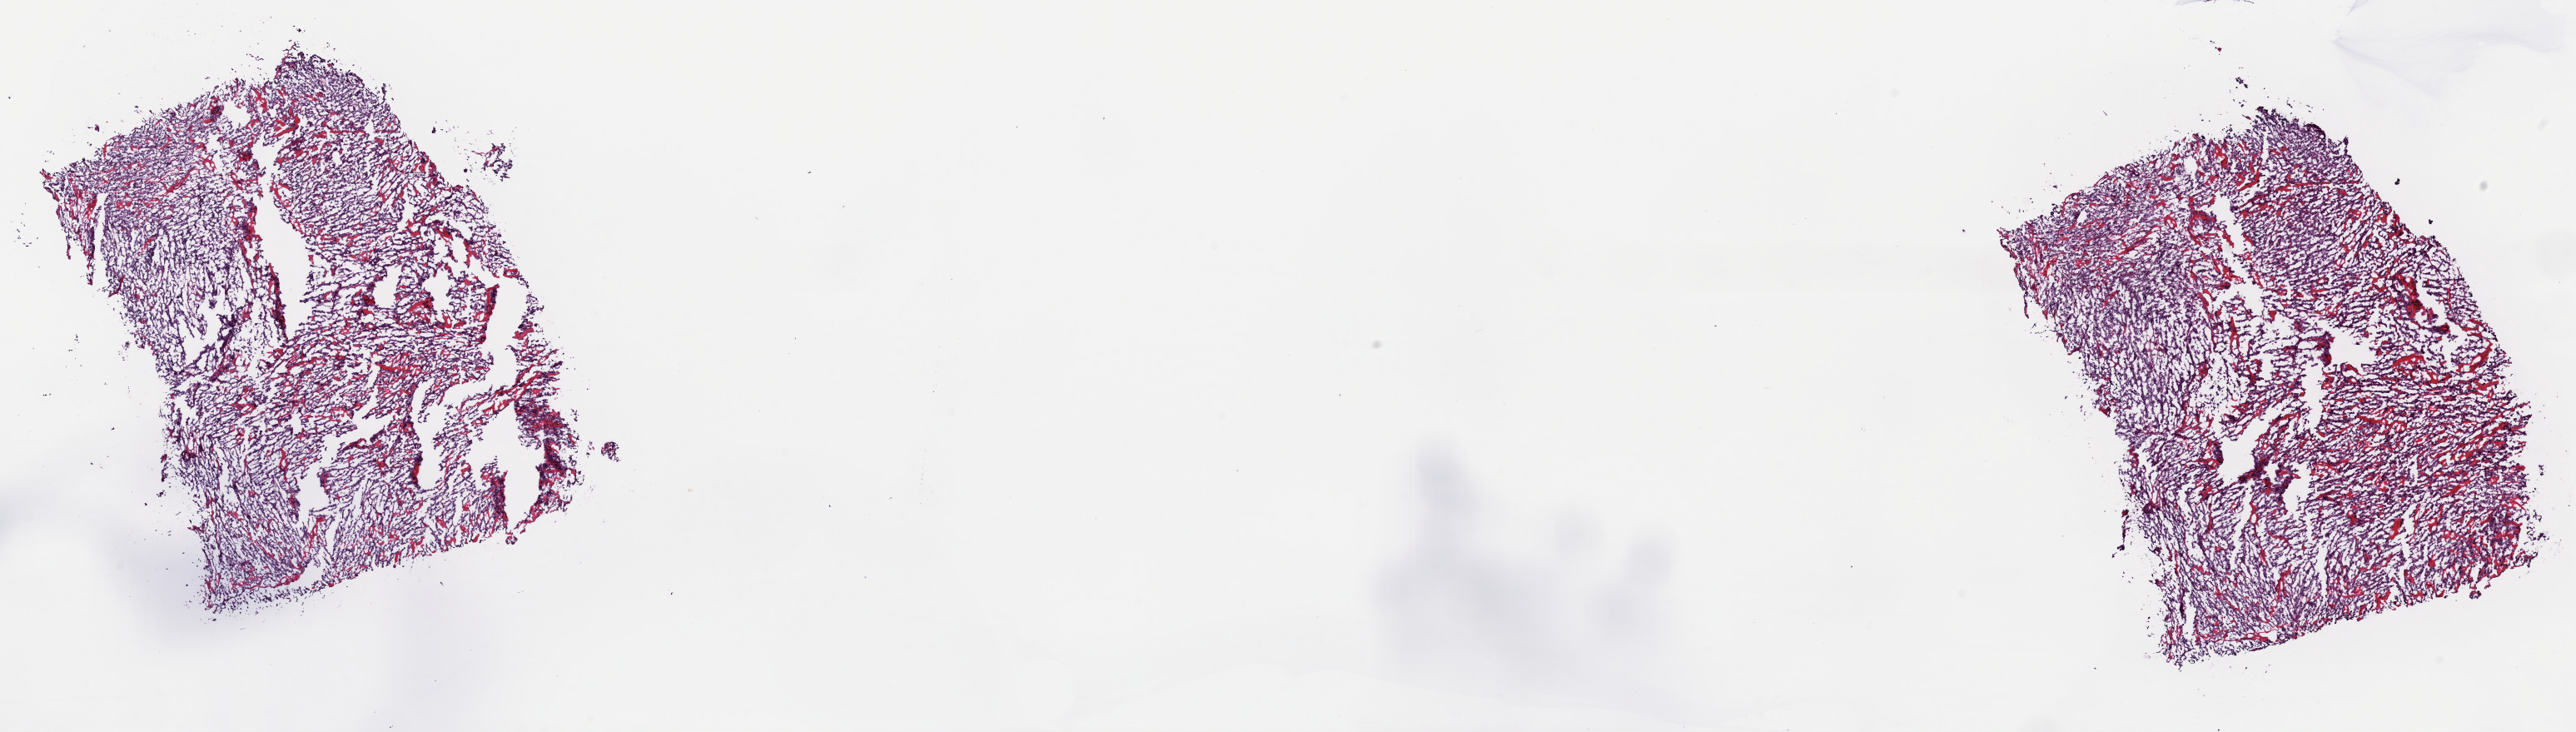
Digitized H&E tissue section (whole slide), low-resolution overview of the scanned area, about 24.4 x 6.9 mm (slide scanned at 40x); frozen section from the top of the tissue portion; skin, primary tumour sample. Male patient; age at initial diagnosis 24 years. Pathologist review of this section (percent, as recorded): tumour cells 85%, tumour nuclei 85%, normal cells 0%, stromal cells 15%, necrosis 0%. Infiltration values recorded for this section: lymphocyte infiltration 2%, monocyte infiltration 1%, neutrophil infiltration 0%.
Histologic diagnosis: Malignant melanoma, NOS. AJCC pathologic stage: IV (6th edition).